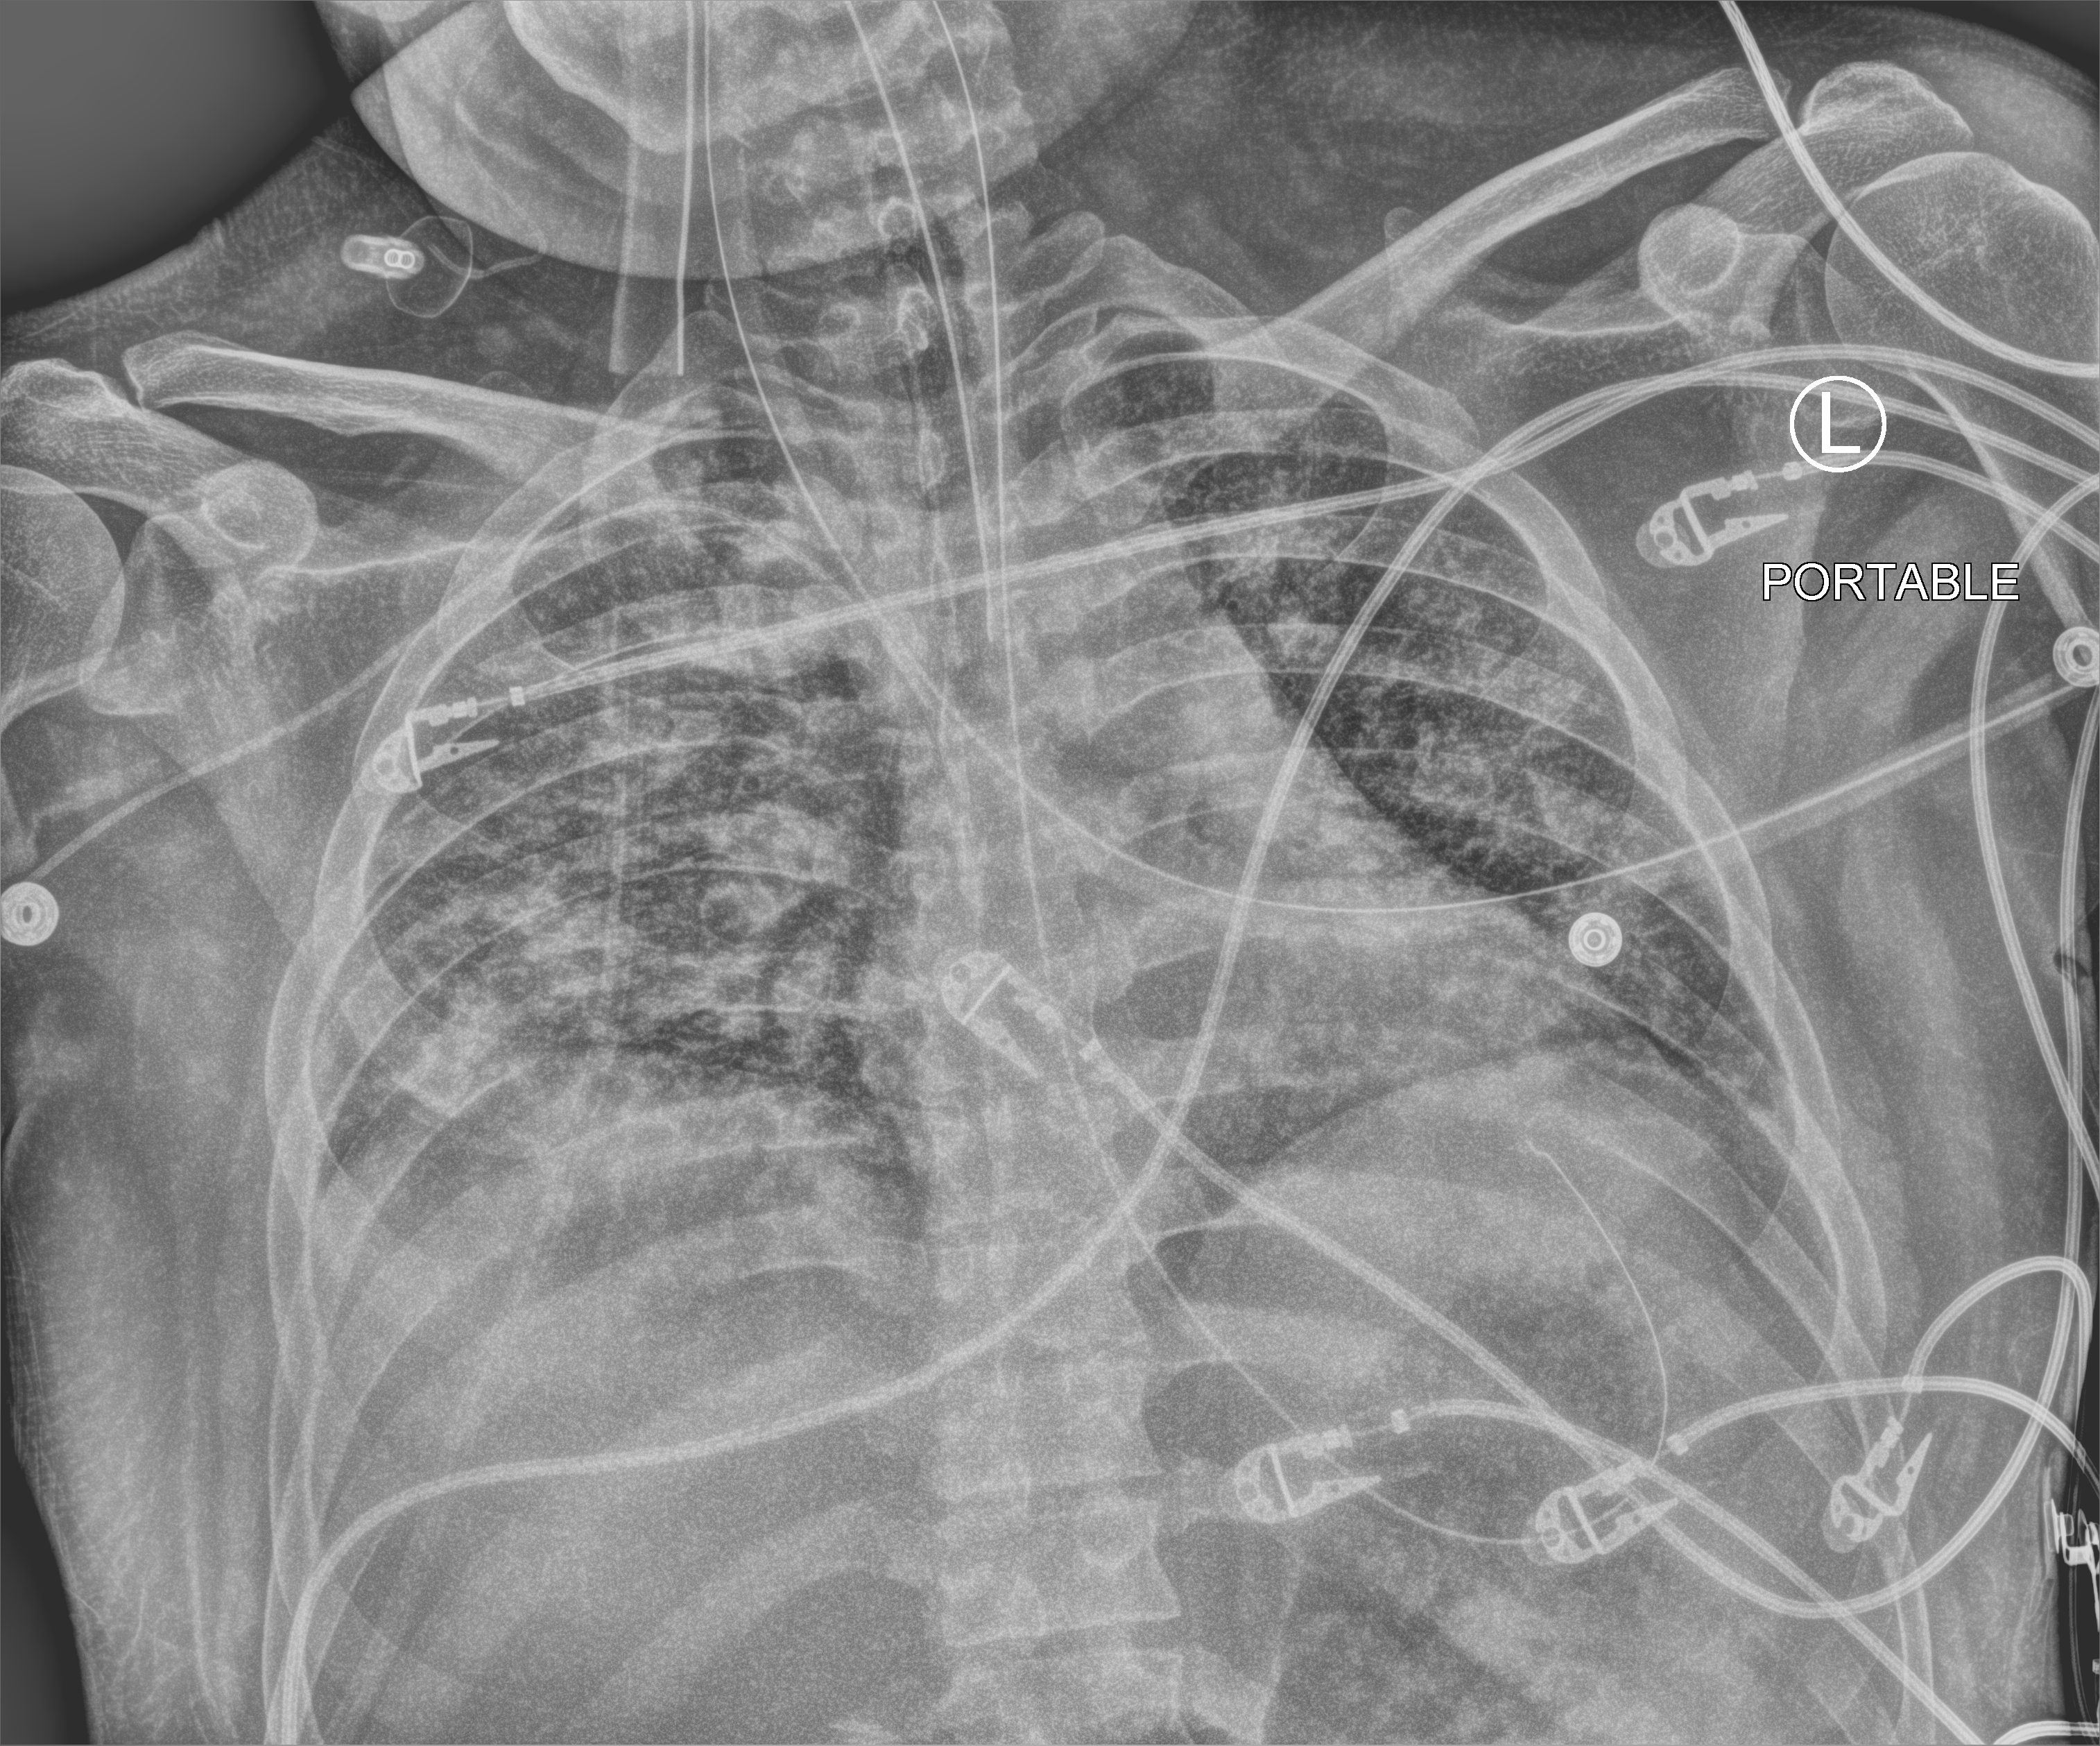
Portable chest radiograph; anteroposterior (AP) projection. Patient hospitalised with COVID-19; male, aged 18–59 years.
From the hospital-stay record, not from the radiograph (when in the stay this image was taken is not recorded):
- COPD (admission record): no
- admitted to intensive care during this hospital stay: yes
- hypertension (admission record): no